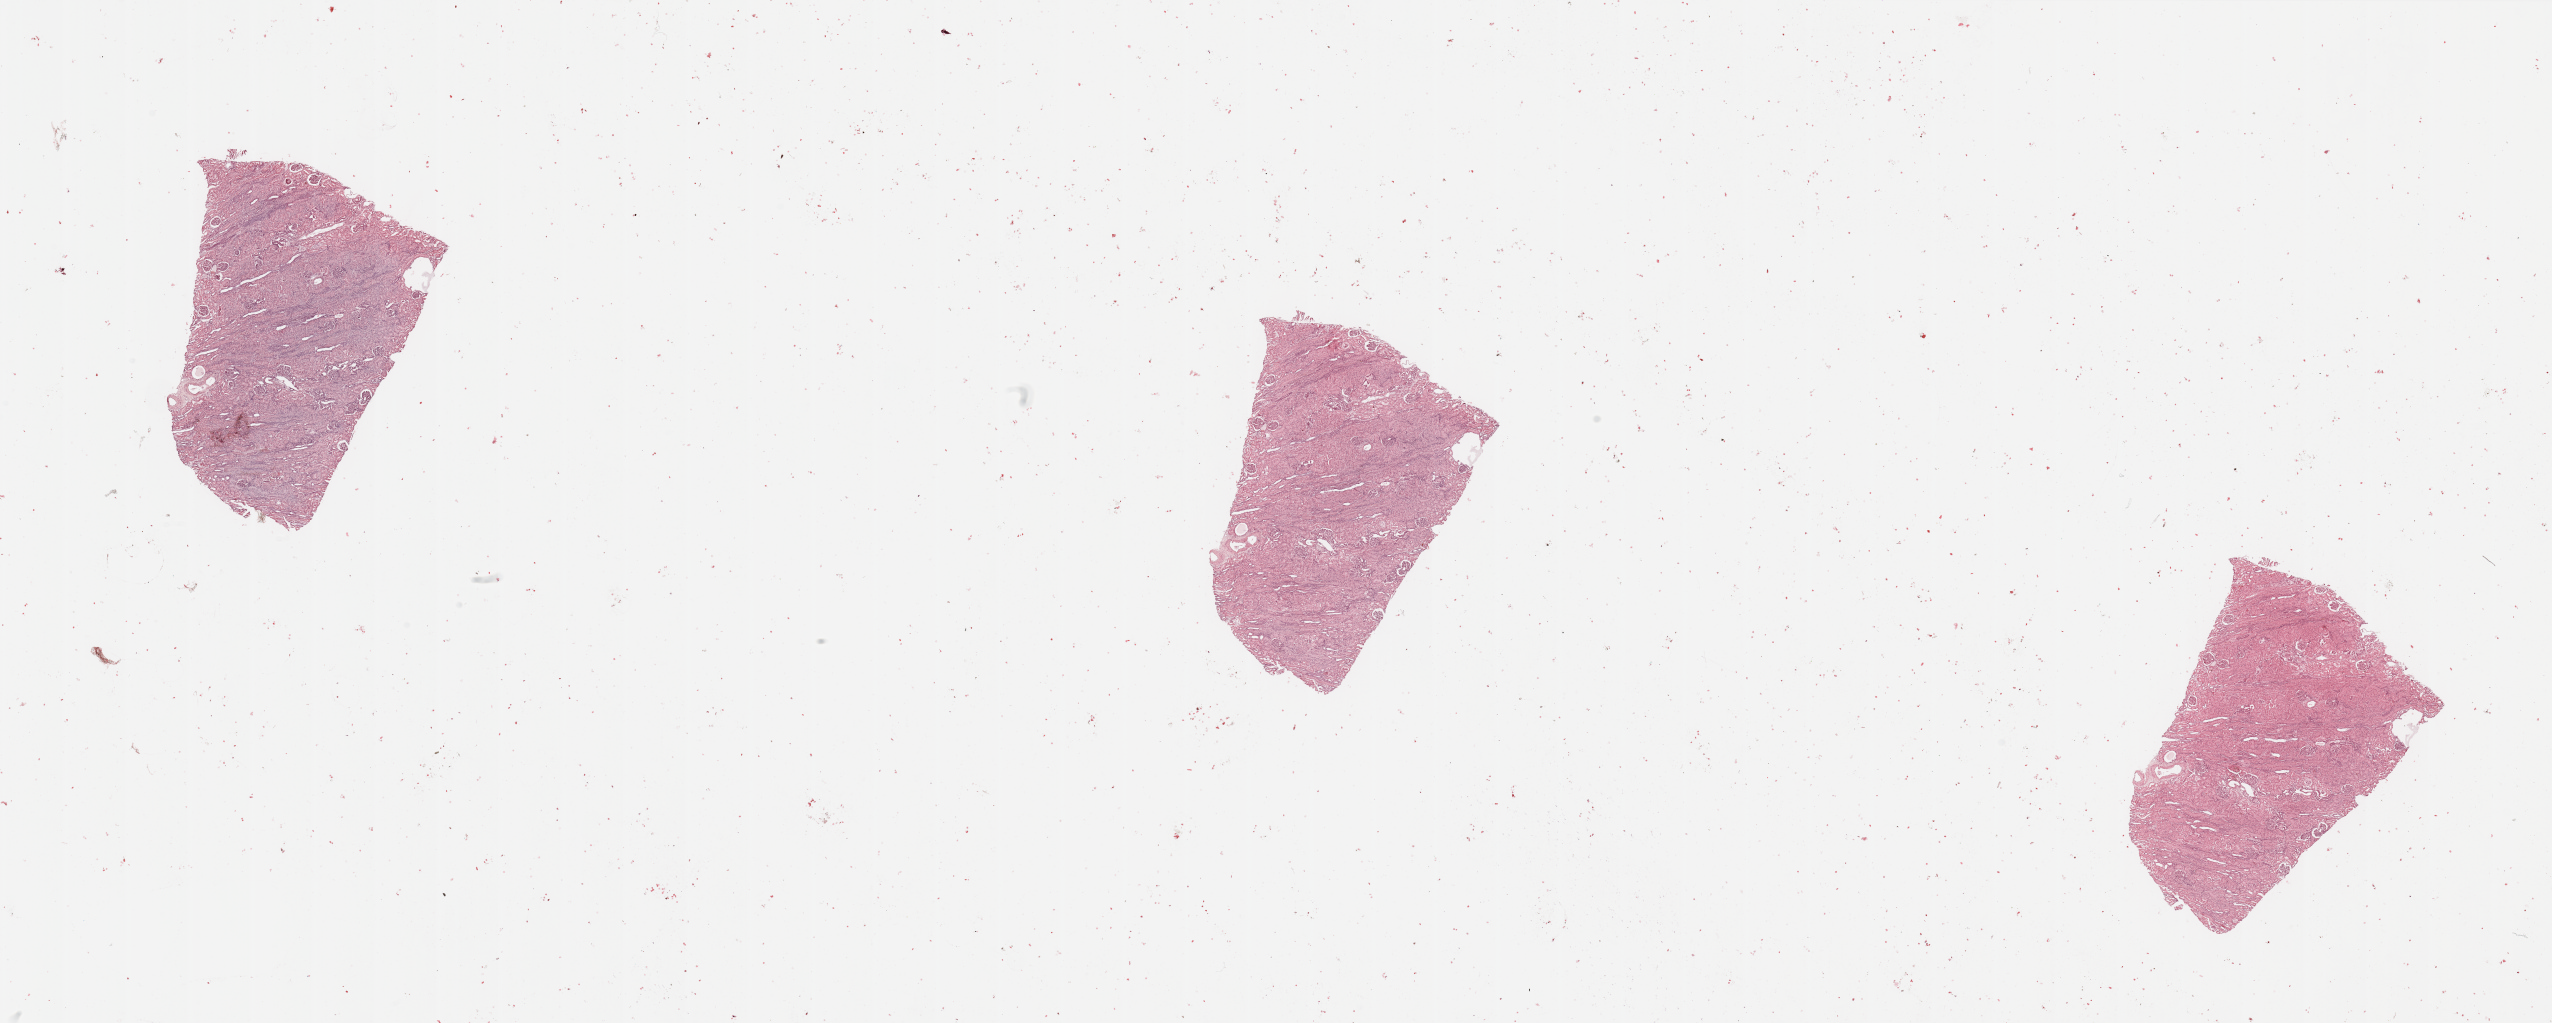
Whole-slide histology image, H&E — shown as a low-resolution overview of the whole scanned area (about 40.4 x 16.2 mm, slide scanned at 20x); normal (non-tumour) tissue sample, sampled site: kidney. 64-year-old female patient.
This section: normal (non-tumour) tissue from the same patient. Patient diagnosis: Renal cell carcinoma, NOS.